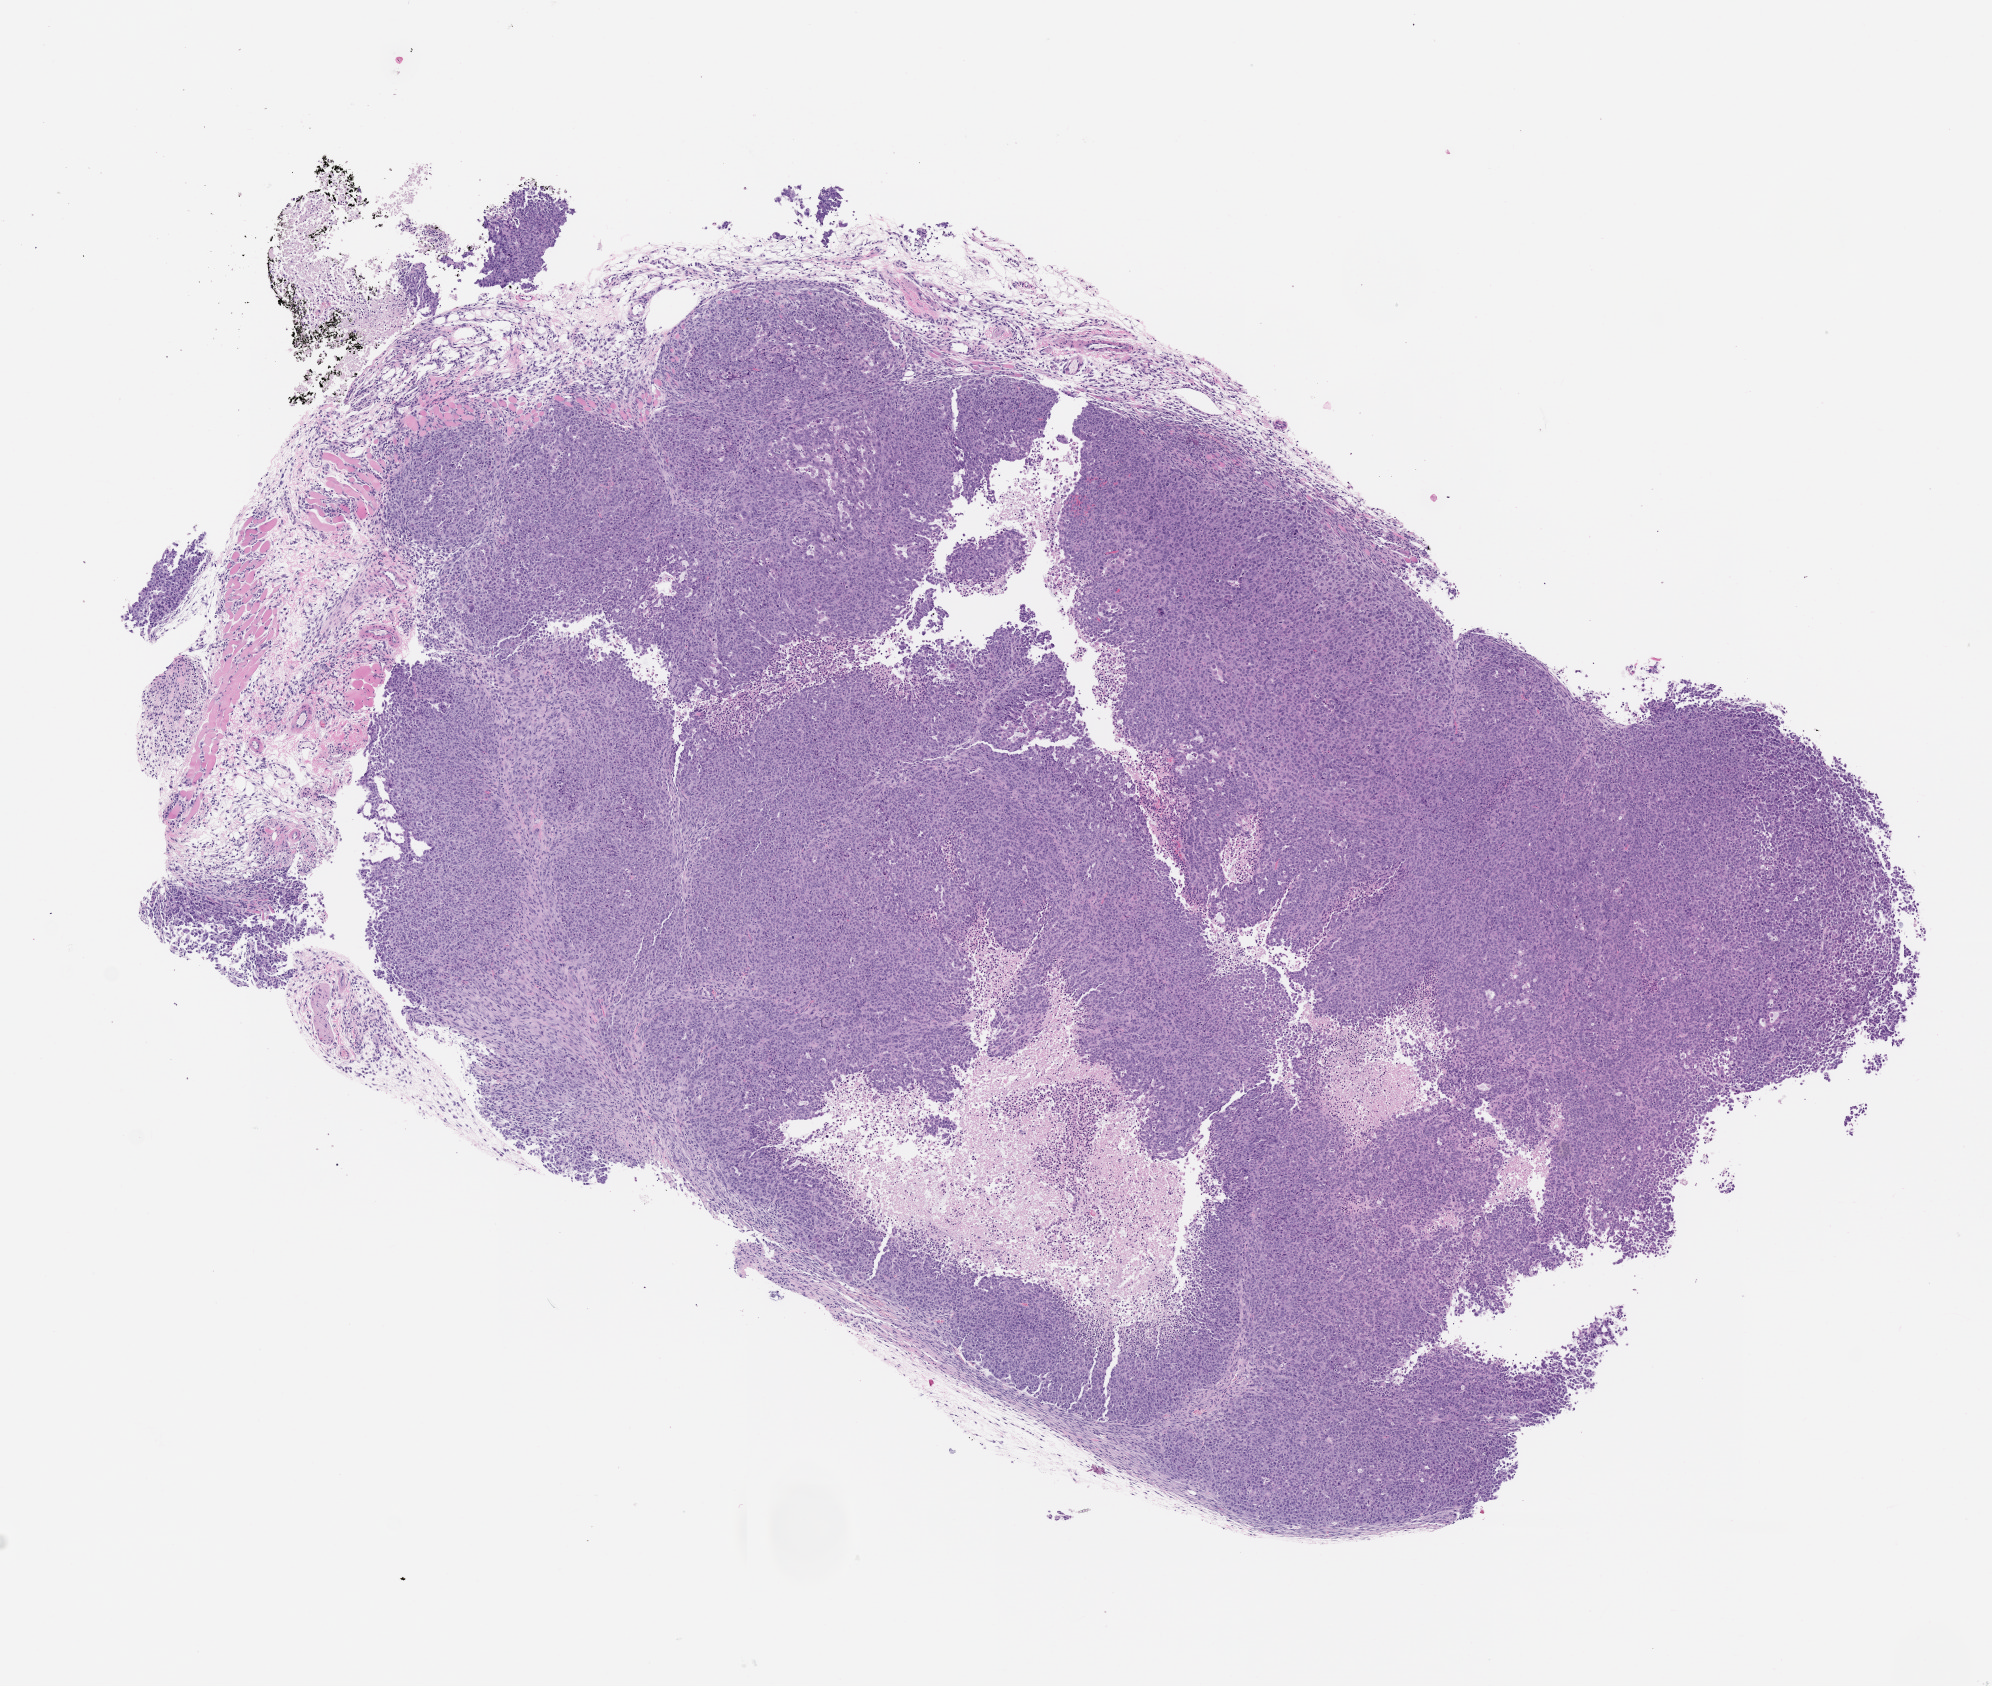
Whole-slide image, haematoxylin and eosin: patient-derived xenograft (human tumor grown in a mouse), passage 2 — low-resolution overview of the scanned area, about 8.0 x 6.8 mm; FFPE section; originating tumor site category: pancreas.
Originating patient diagnosis: Pancreatic Adenocarcinoma.